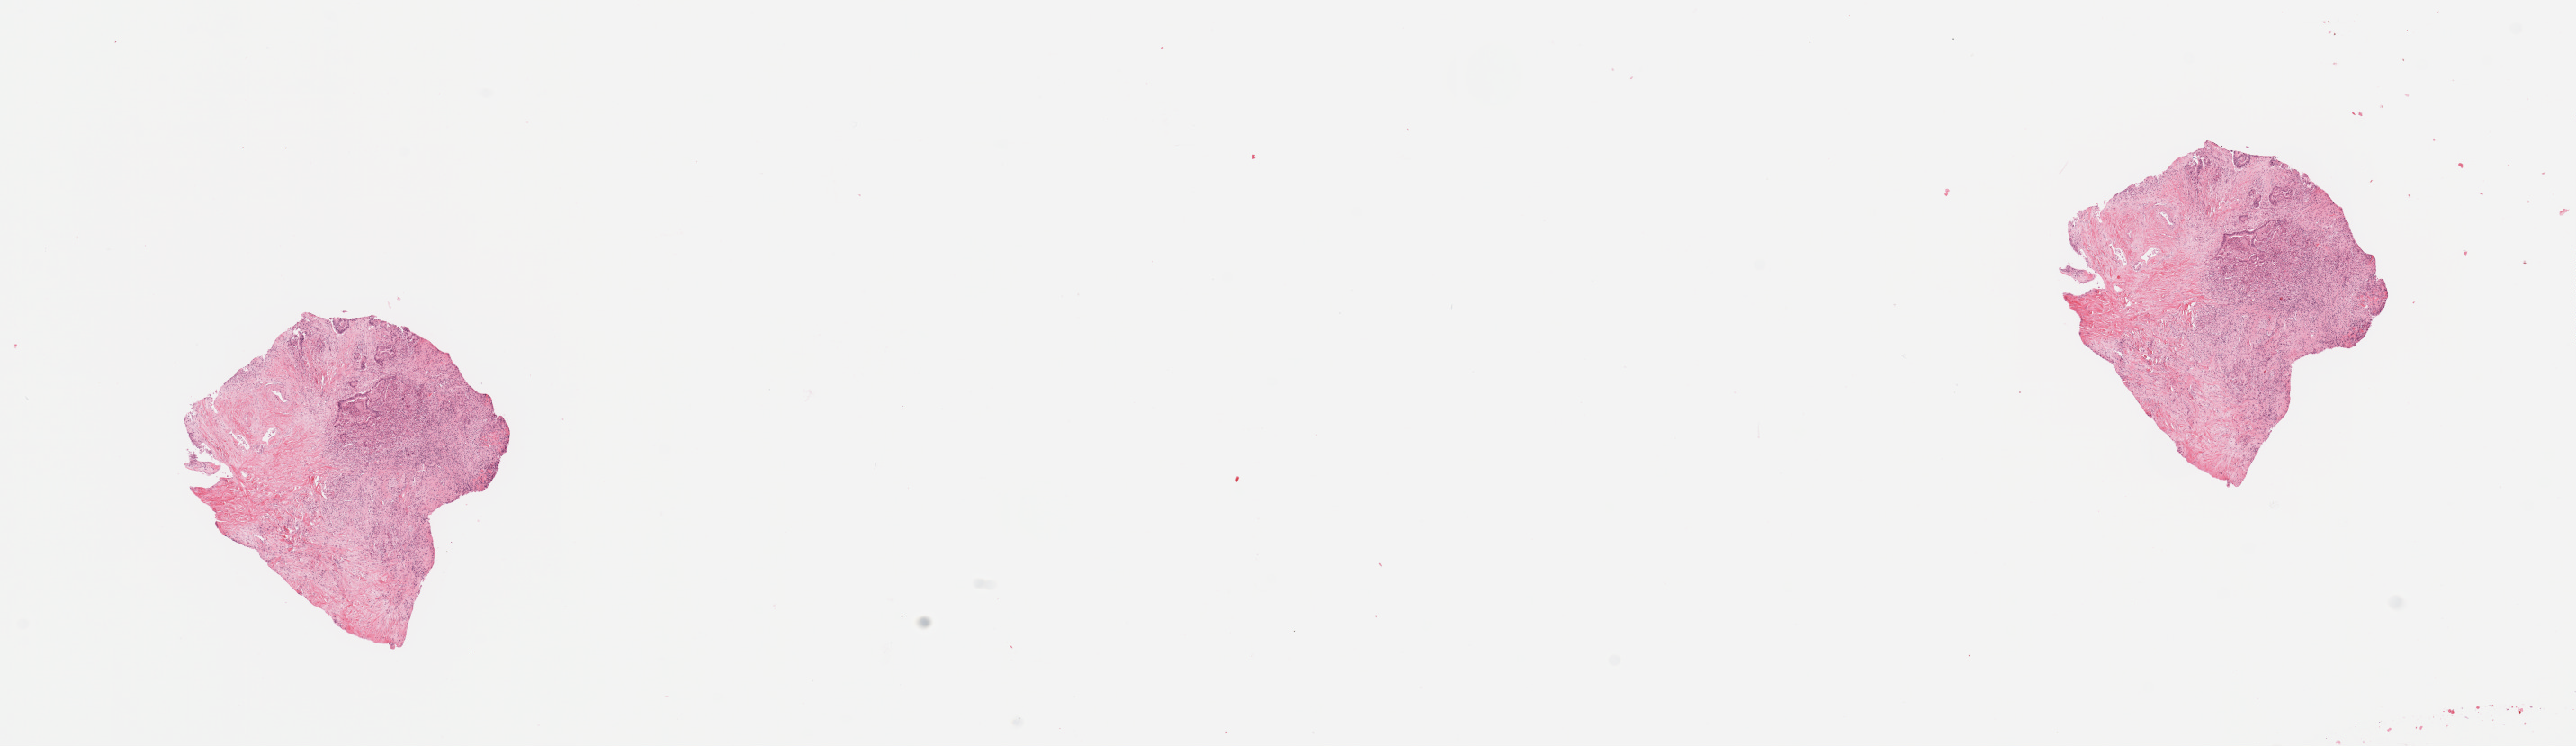
H&E-stained whole-slide image — low-resolution overview of the scanned area, about 22.6 x 6.6 mm, tumour tissue sample, sampled site: pancreas. Patient: male, age 75 years. Histologic grade: G2 (moderately differentiated). Composition of this section per pathologist review: tumour nuclei 10%, necrosis 0%.
- histologic diagnosis: Infiltrating duct carcinoma, NOS
- AJCC pathologic stage: III